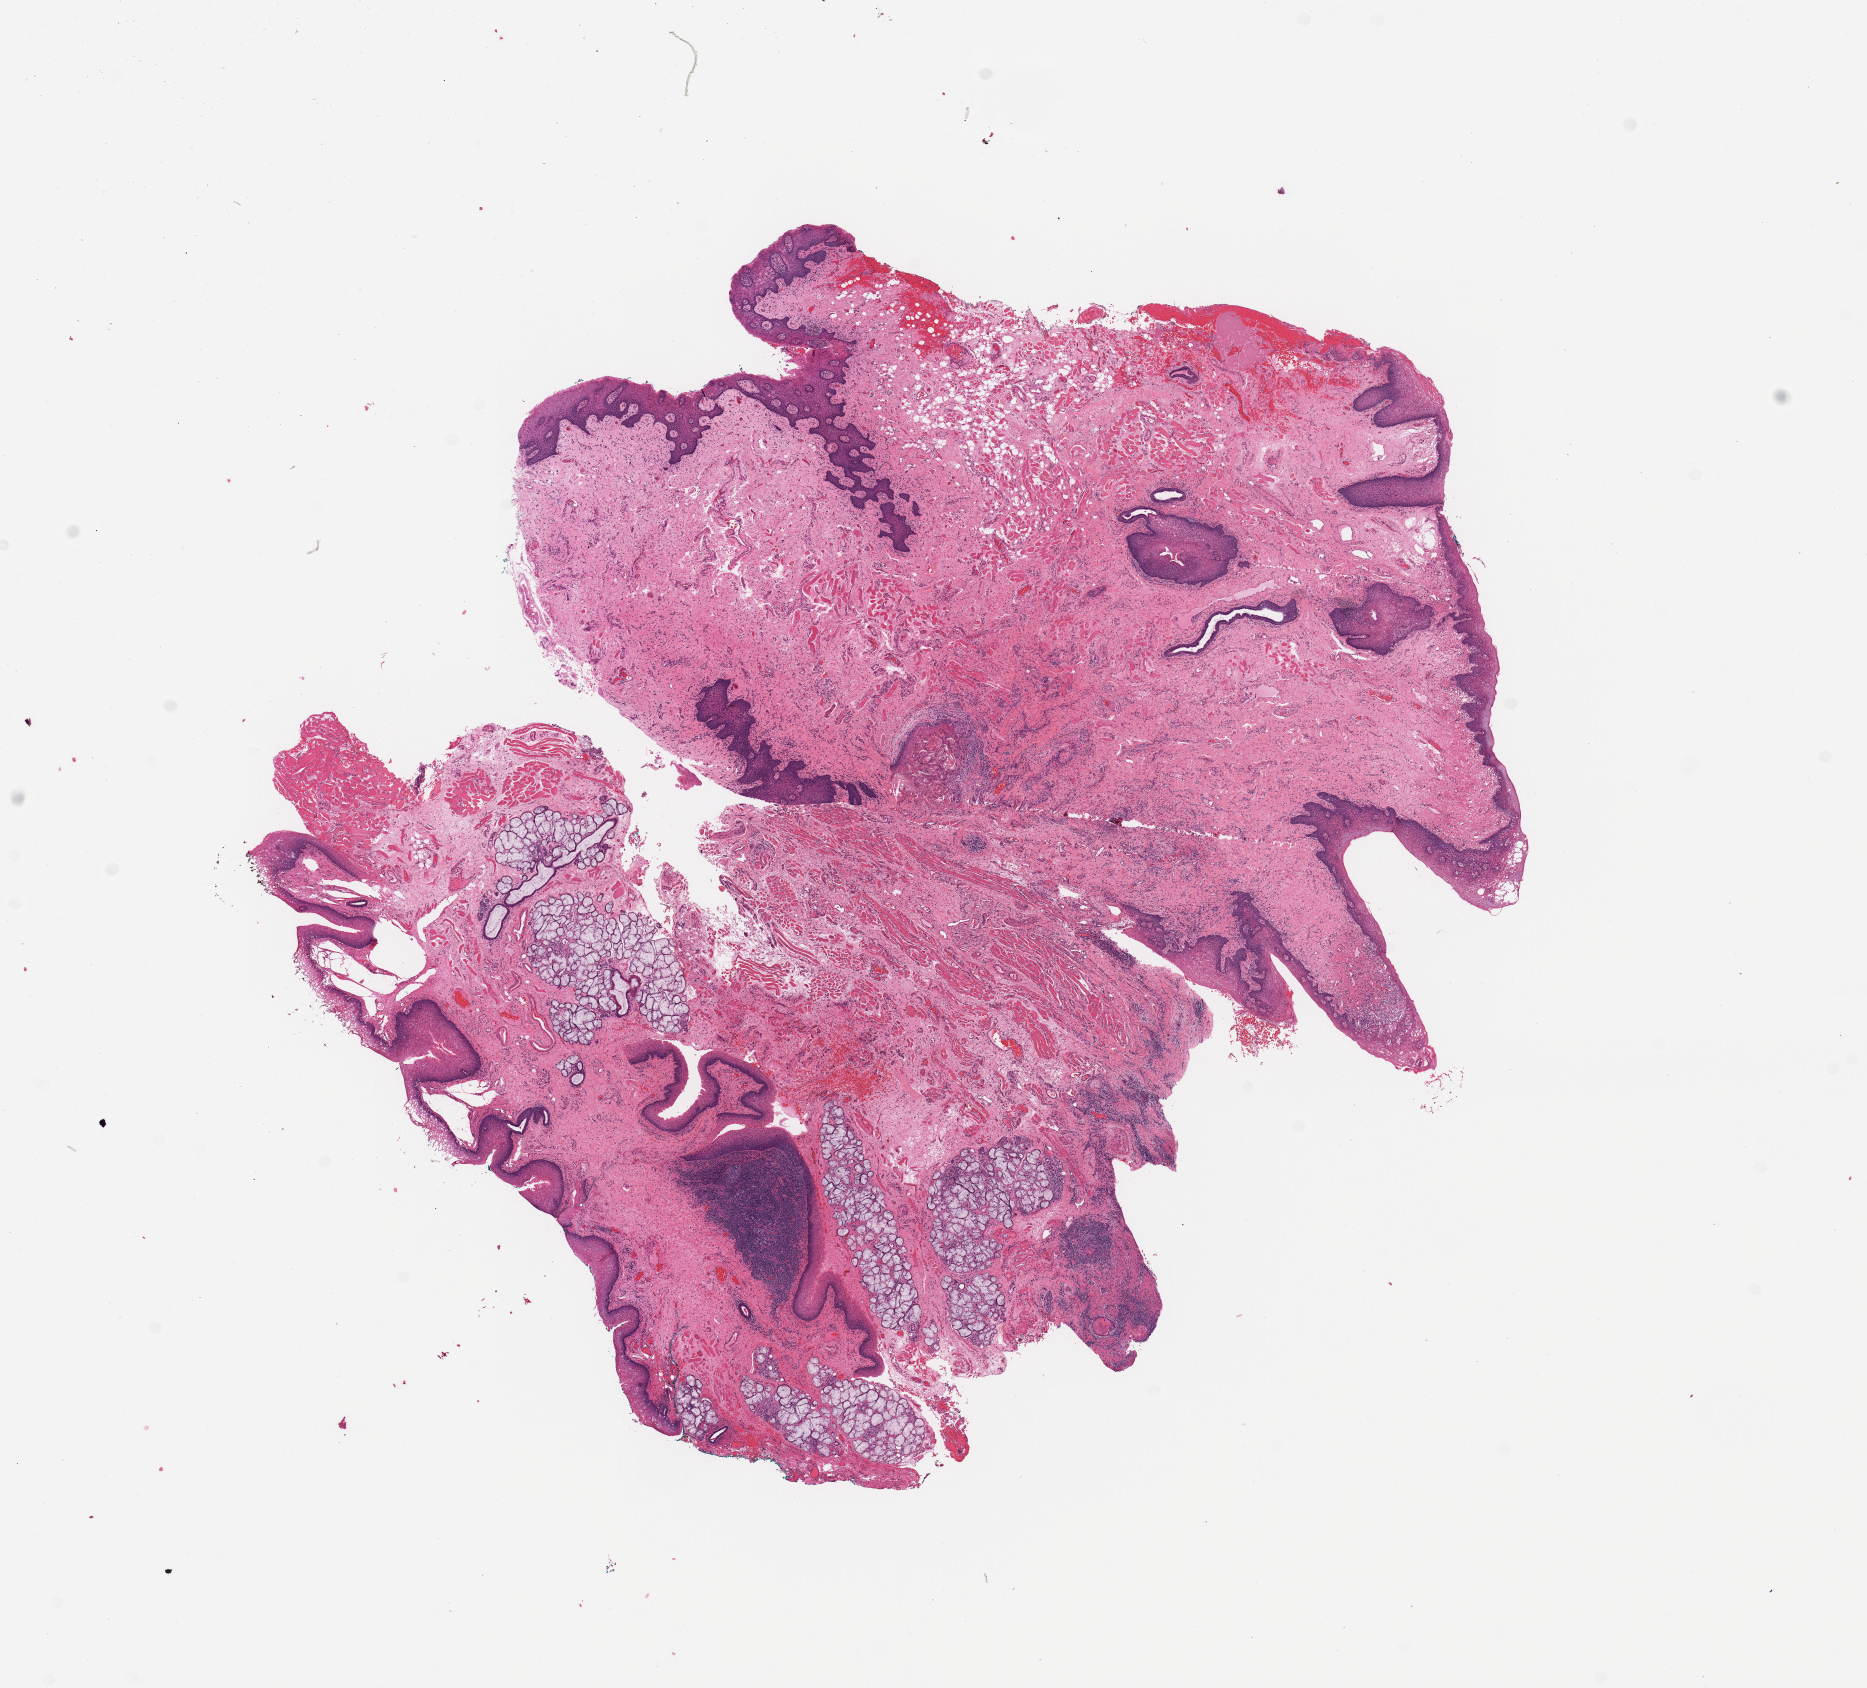
Digitized H&E tissue section (whole slide) — shown as a low-resolution overview of the whole scanned area (about 14.8 x 13.4 mm, from a 20x scan). Normal (non-tumour) tissue sample, sampled site: buccal mucosa. Male, 56 y/o.
• this section: normal (non-tumour) tissue from the same patient
• patient diagnosis: Squamous cell carcinoma, NOS (cheek mucosa)